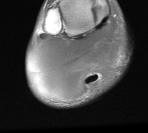
MRI of an extremity soft-tissue mass, one axial slice; position 12 of 76 along the scan axis; MR volume resampled by the dataset authors to the PET/CT grid (not the native acquisition matrix); 3.27 mm slice thickness; 148 × 133 image matrix, field of view 145 × 130 mm. Male patient. Case-level facts recorded for this patient, not image findings: histological type: liposarcoma - round cell; grade: high; site of the primary tumour: right calf.
Outlined on this slice (expert contour drawn on MRI and transferred to this co-registered scan by the dataset authors):
- gross tumour volume (mass): box from (x=29, y=23) to (x=123, y=102) px